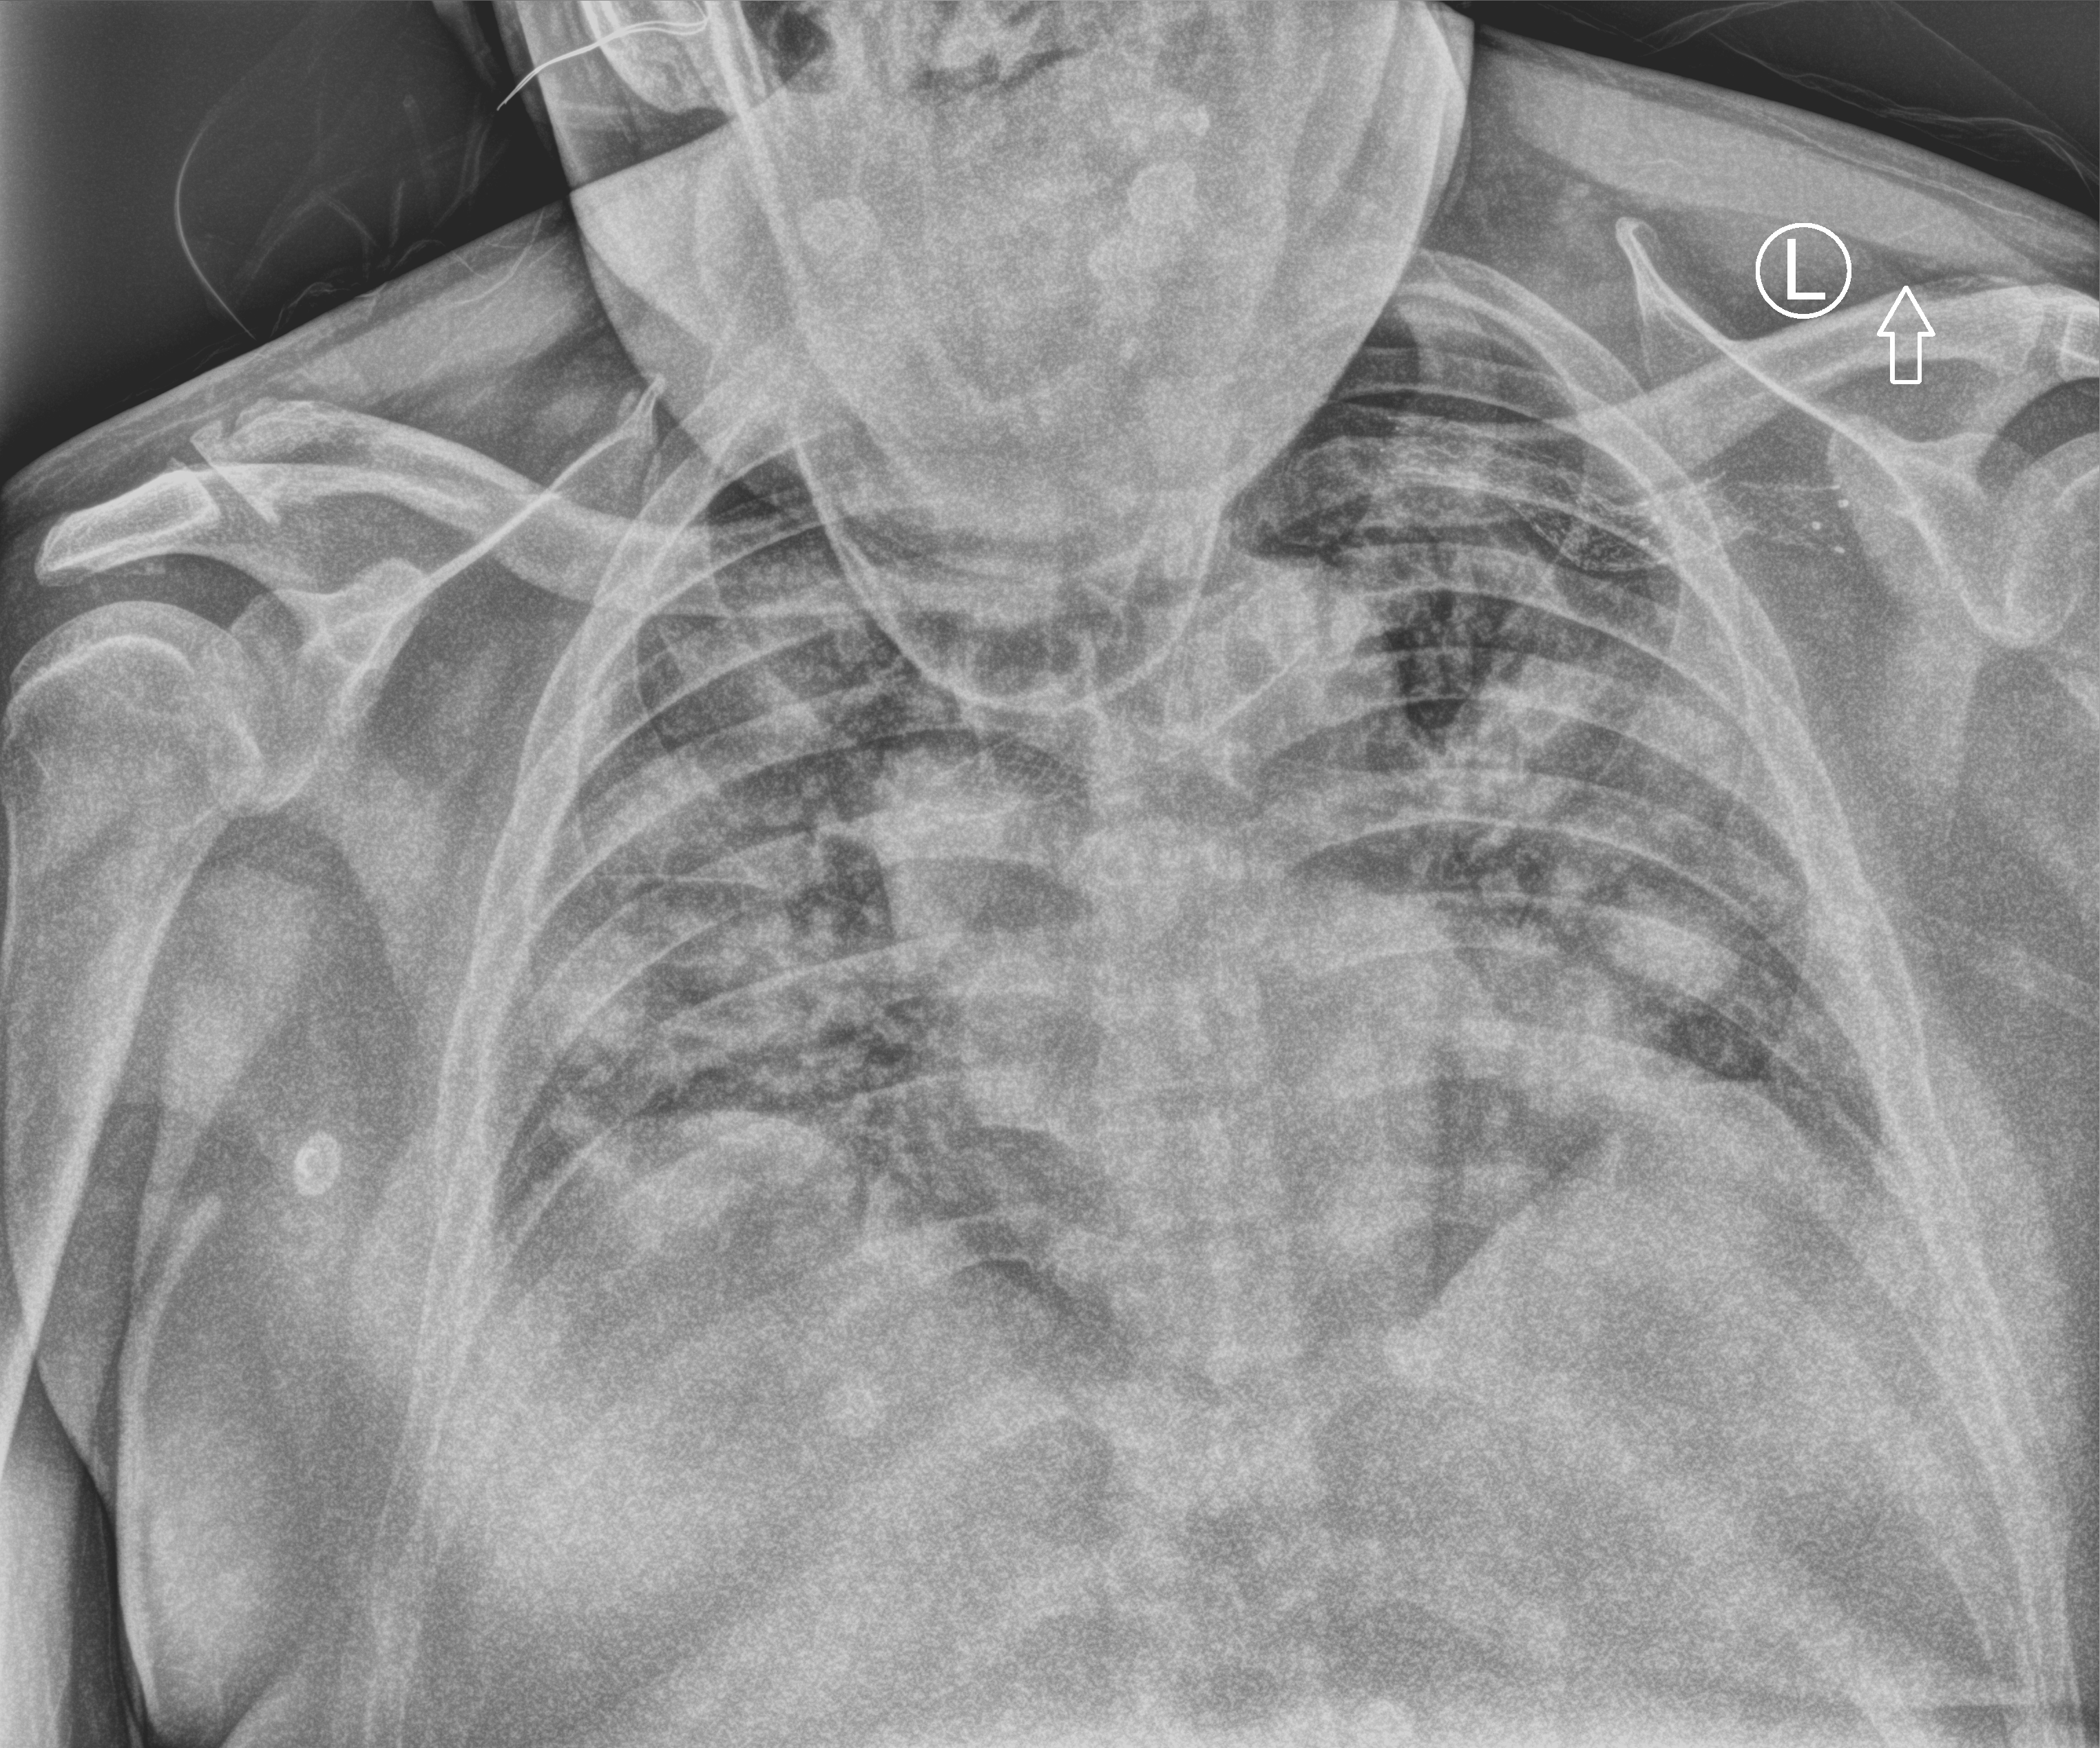
Chest X-ray (portable), anteroposterior (AP) projection. Male patient hospitalised with COVID-19, age 18–59 years.
Hospital-stay facts (about this admission, not read from this image; timing relative to this image not recorded): smoking status (admission record): never.